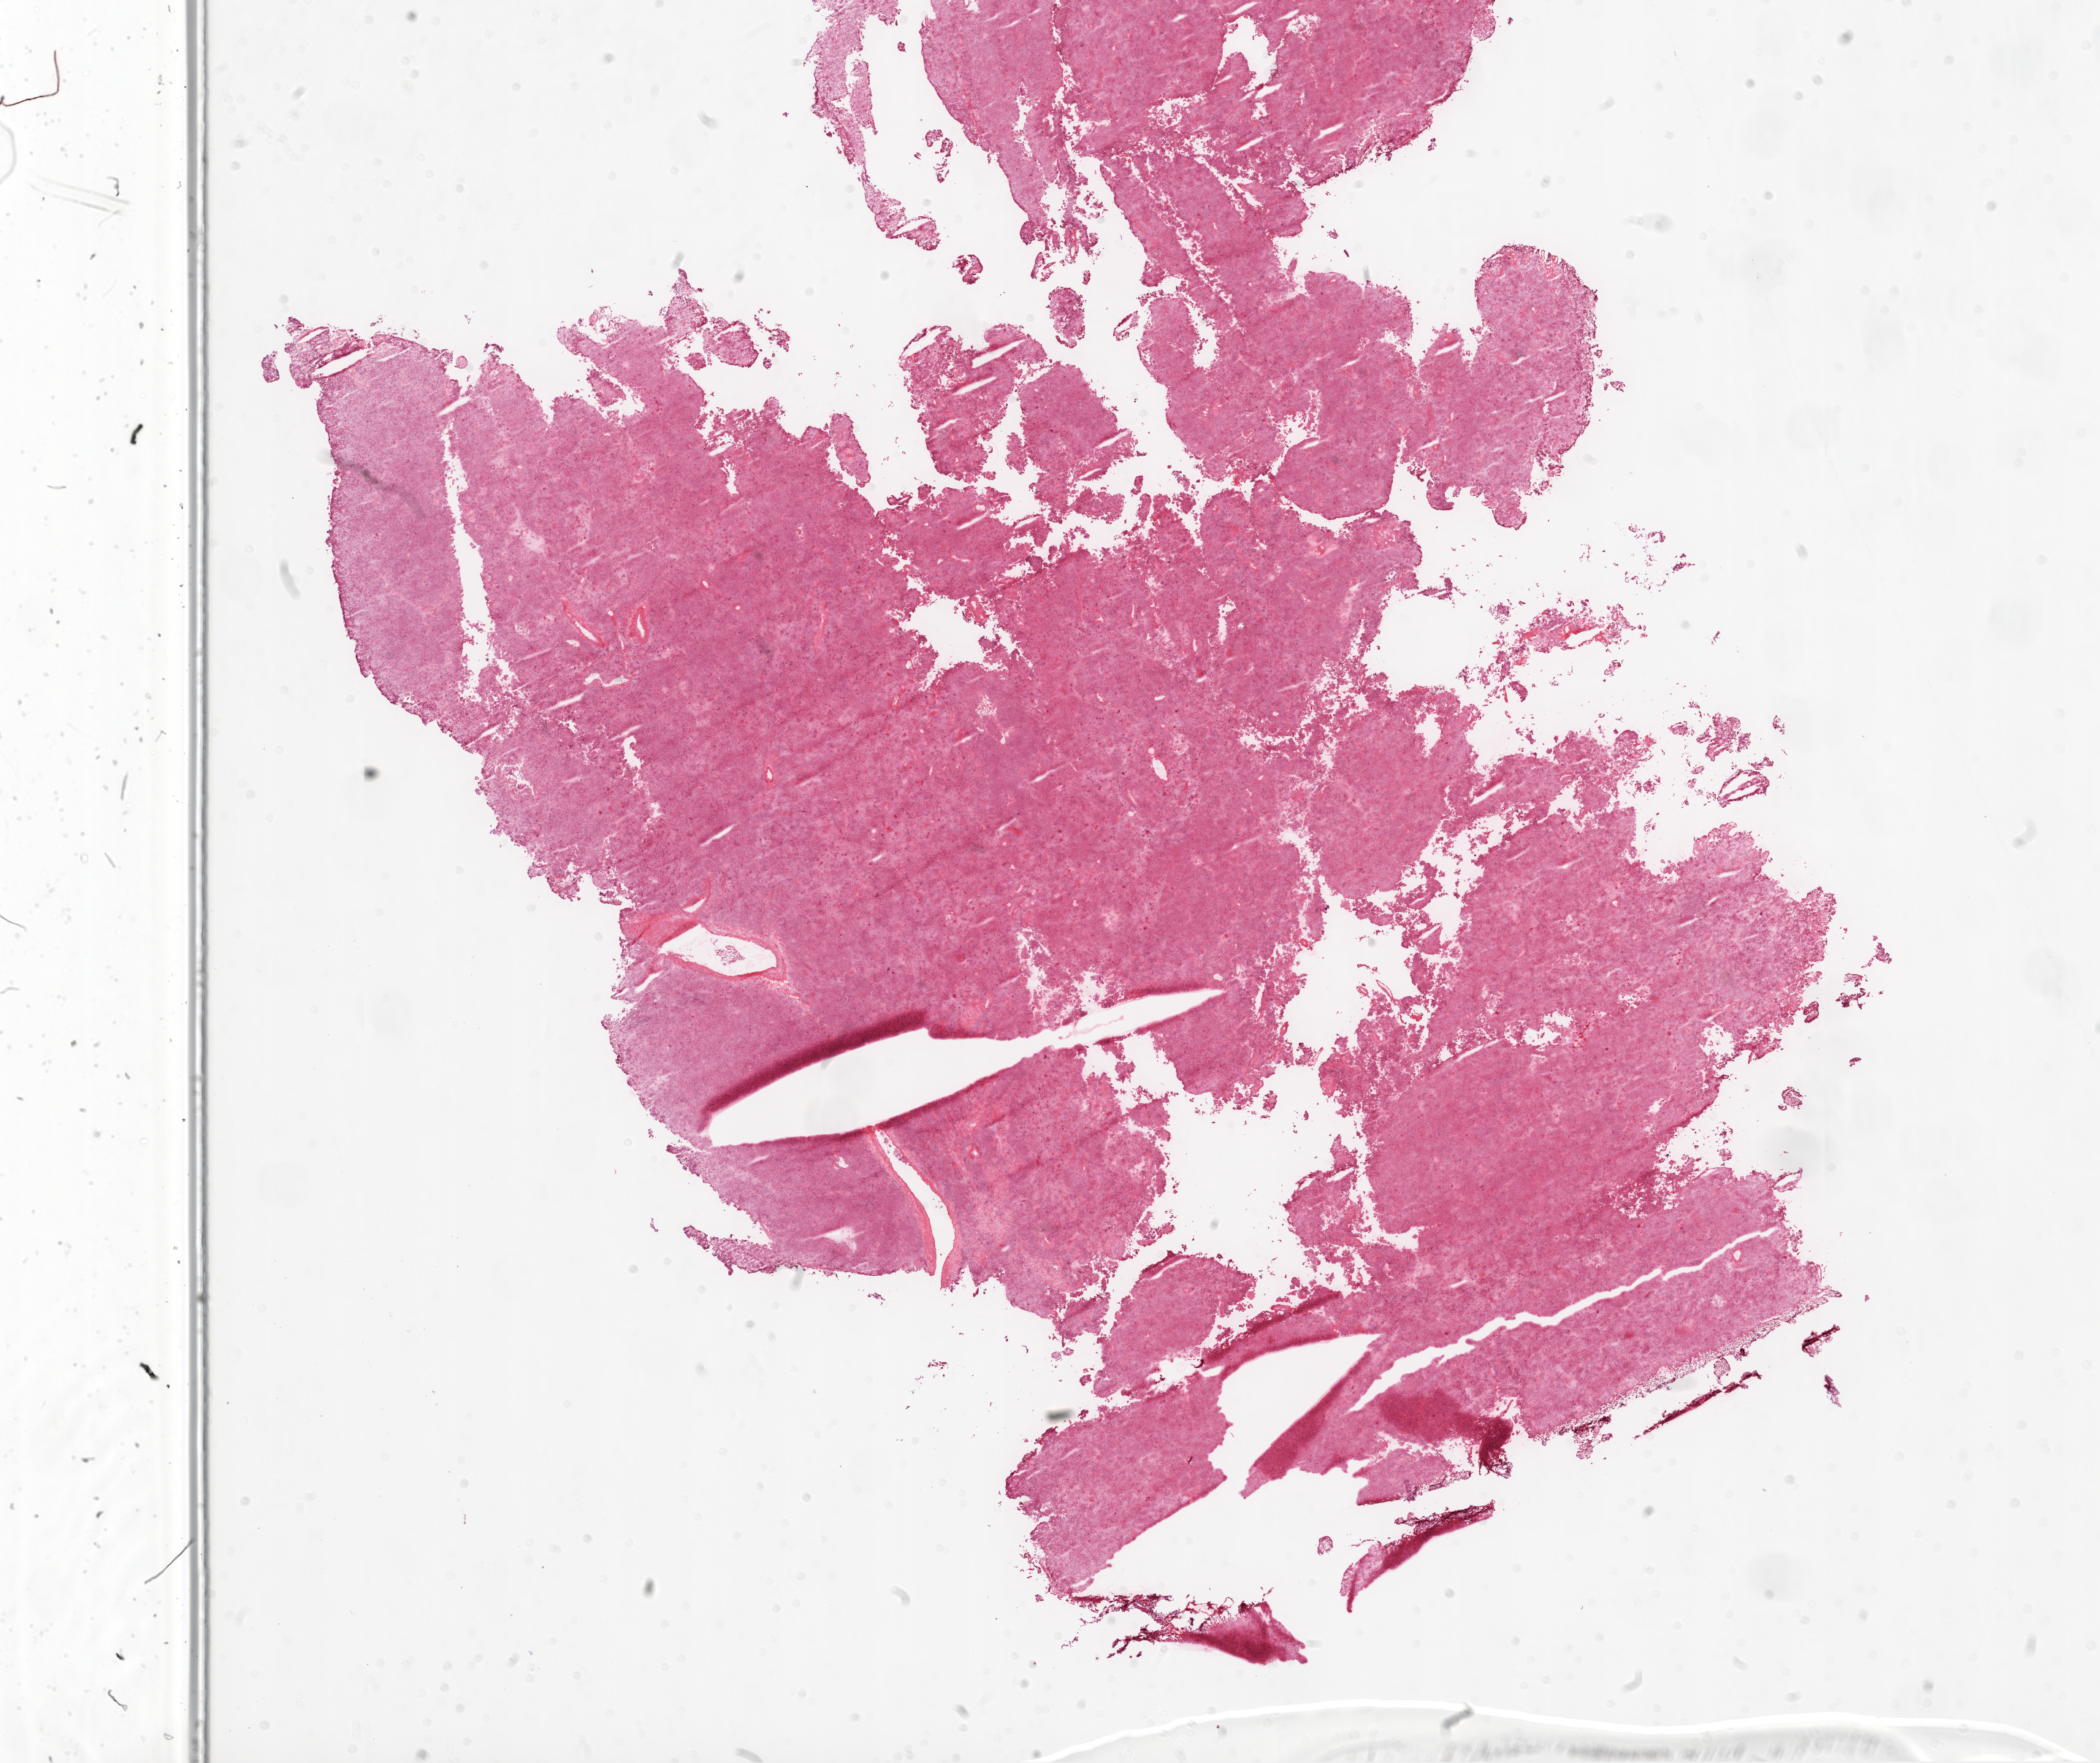
H&E whole-slide image, a low-resolution overview of the entire scanned area, about 23.1 x 19.4 mm, frozen section from the top of the tissue portion, primary tumour sample from the ovary. Female patient; age at initial diagnosis 77 years. Histologic grade: G3 (poorly differentiated). Slide review estimates, as recorded: tumour cells 90%, tumour nuclei 90%, normal cells 1%, stromal cells 9%, necrosis 0%.
* laterality: right
* FIGO stage: IIB
* diagnosis: Serous cystadenocarcinoma, NOS